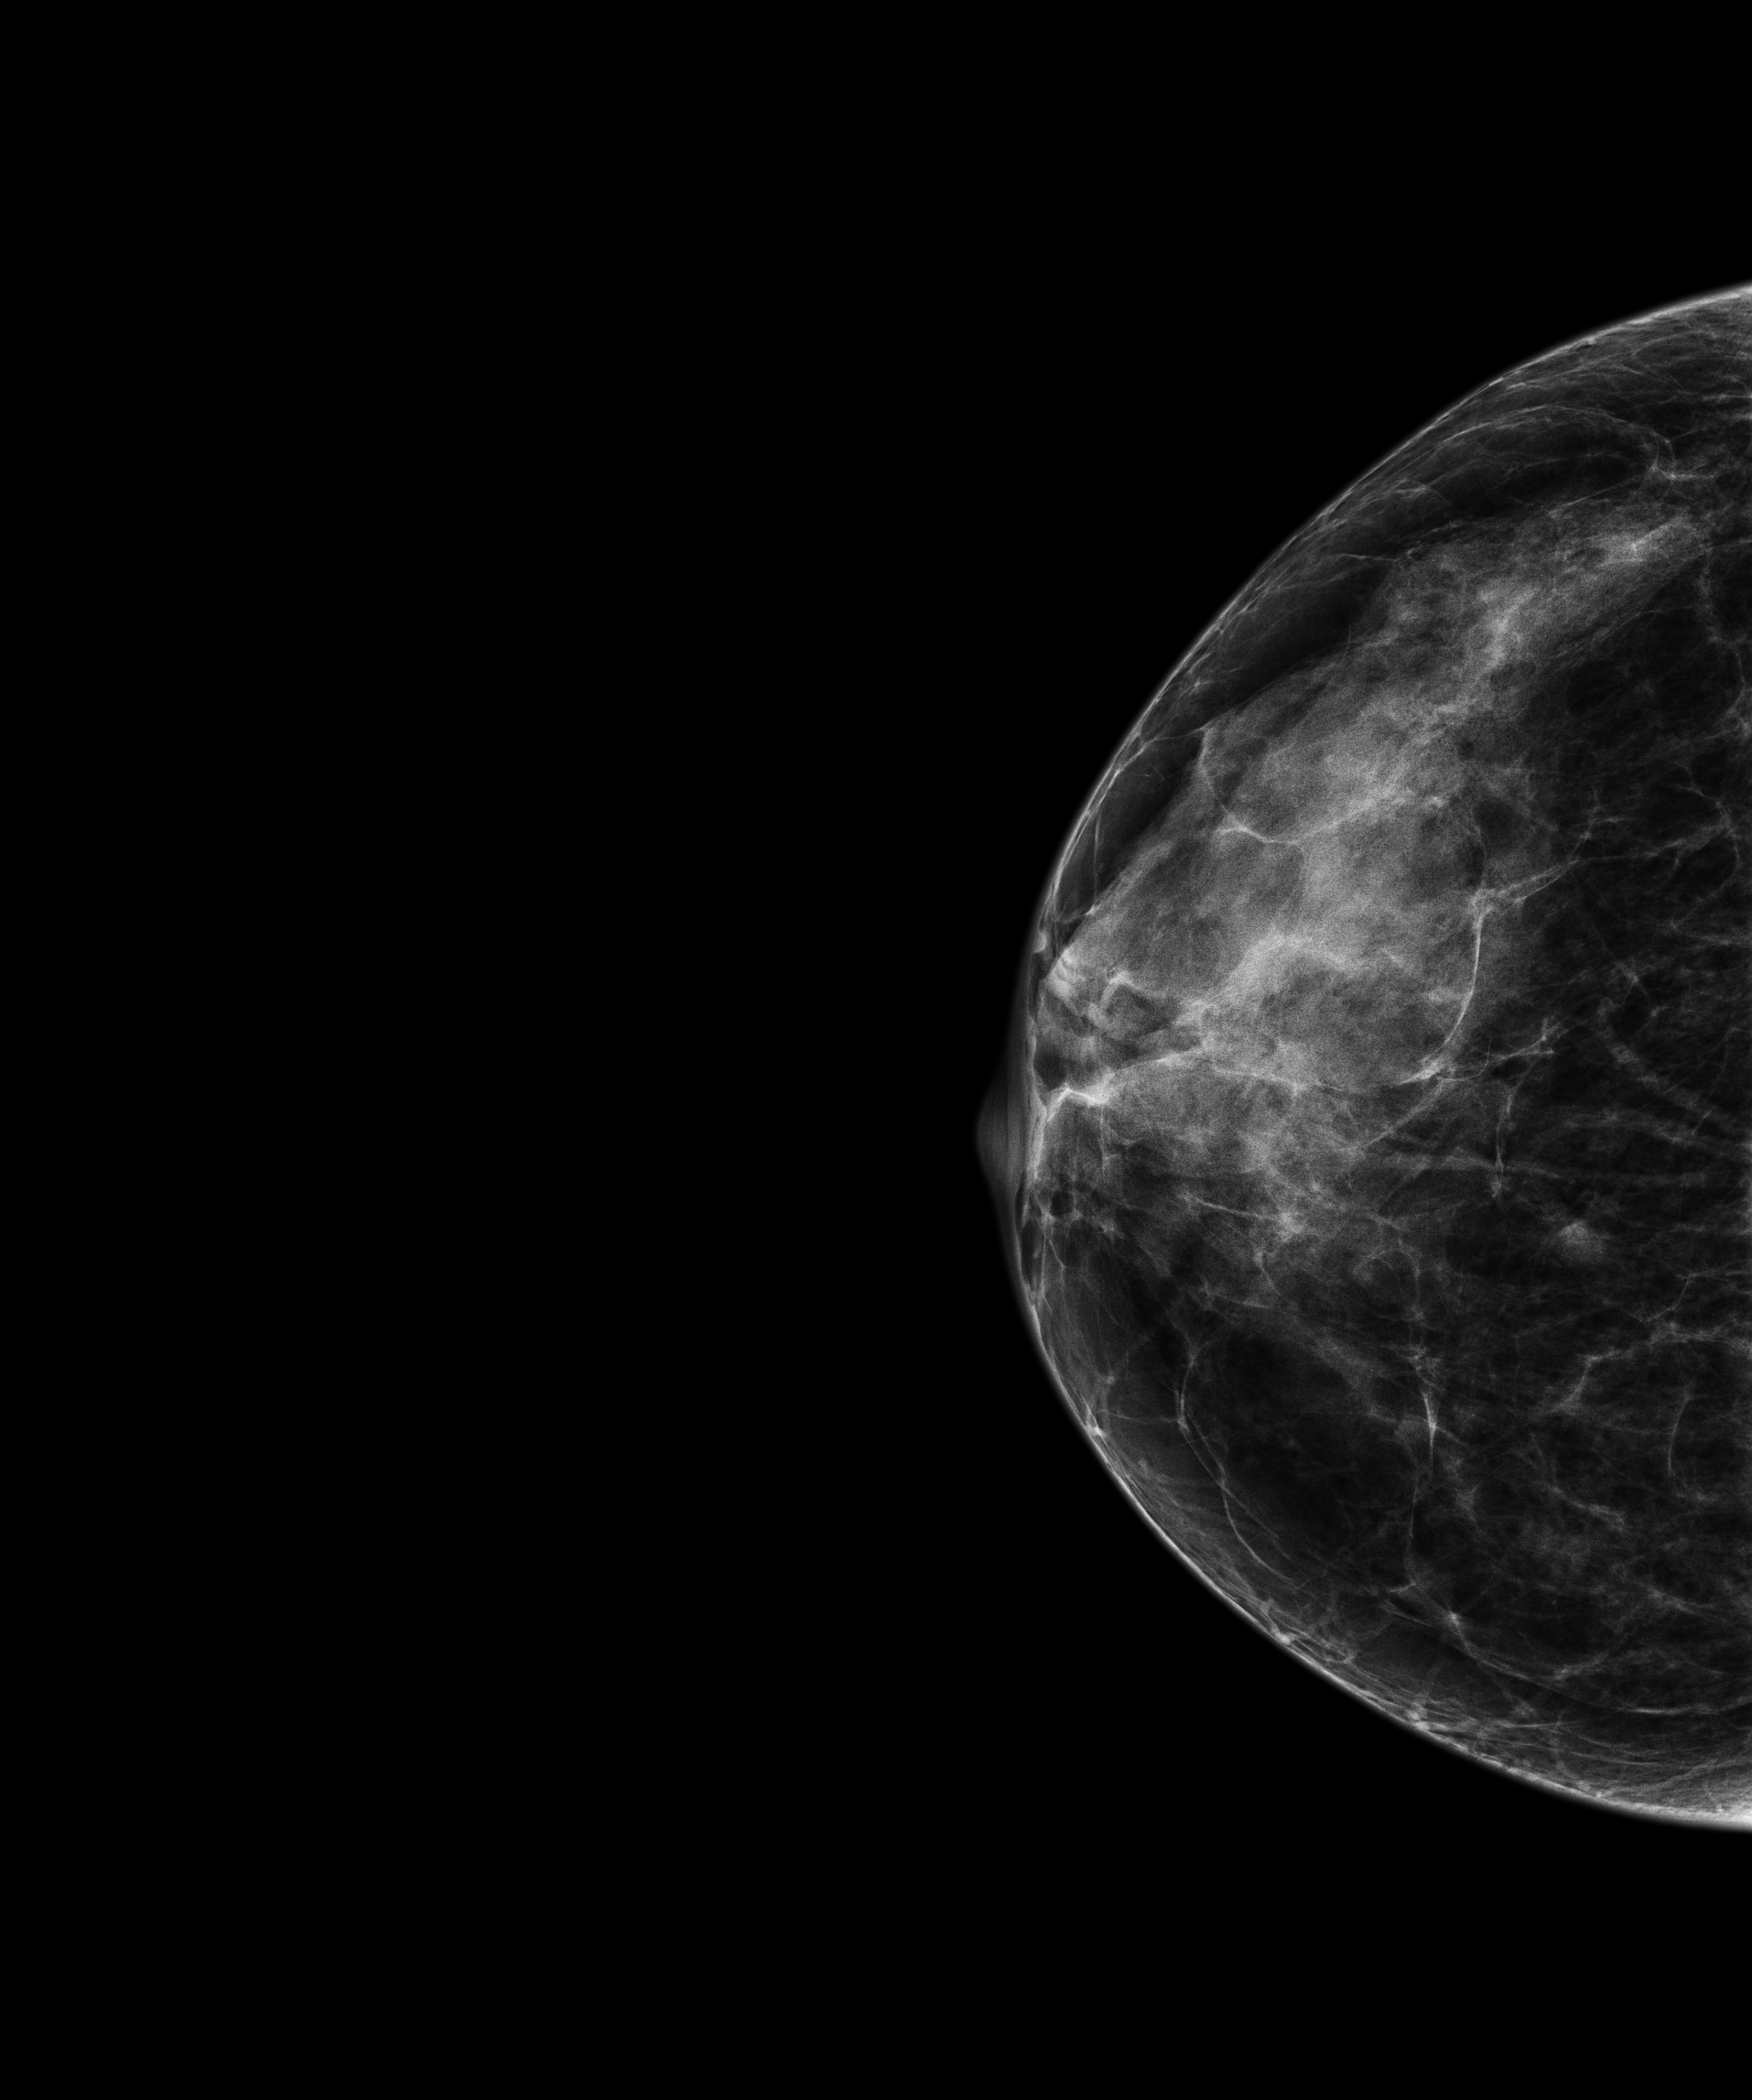
Screening examination, compressed breast thickness 28.6 mm. Patient: female, 48 years.
Image type: full-field digital mammogram. Breast: right. Projection: craniocaudal (CC) view.